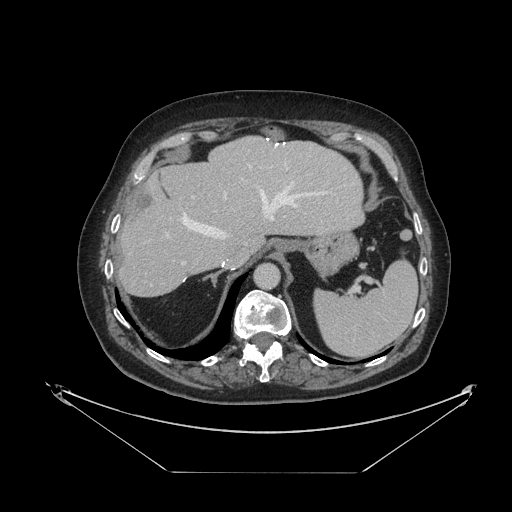
Contrast-enhanced abdominal CT, one axial slice. Position 81 of 121 along the scan axis. Intravenous contrast given. Soft-tissue window (W 400 / L 40 HU). 2.5 mm slice thickness. 512 × 512 image matrix, field of view 500 × 500 mm. Male patient, age 68 years. From the clinical record (not read from this slice): diagnosis: colorectal cancer liver metastases, imaged before liver resection; multiple liver metastases: no; largest metastasis: 4 cm; disease in both lobes: no.
Outlined on this slice (expert manual segmentation):
- hepatic veins: bounding box (x1, y1, x2, y2) in pixels: (169, 144, 332, 237)
- liver: (121, 138, 363, 296)
- planned liver remnant (the part of the liver to remain after resection): (121, 137, 363, 296)
- portal vein (with intrahepatic branches): (167, 191, 227, 265)
- liver metastasis: (130, 187, 154, 220)